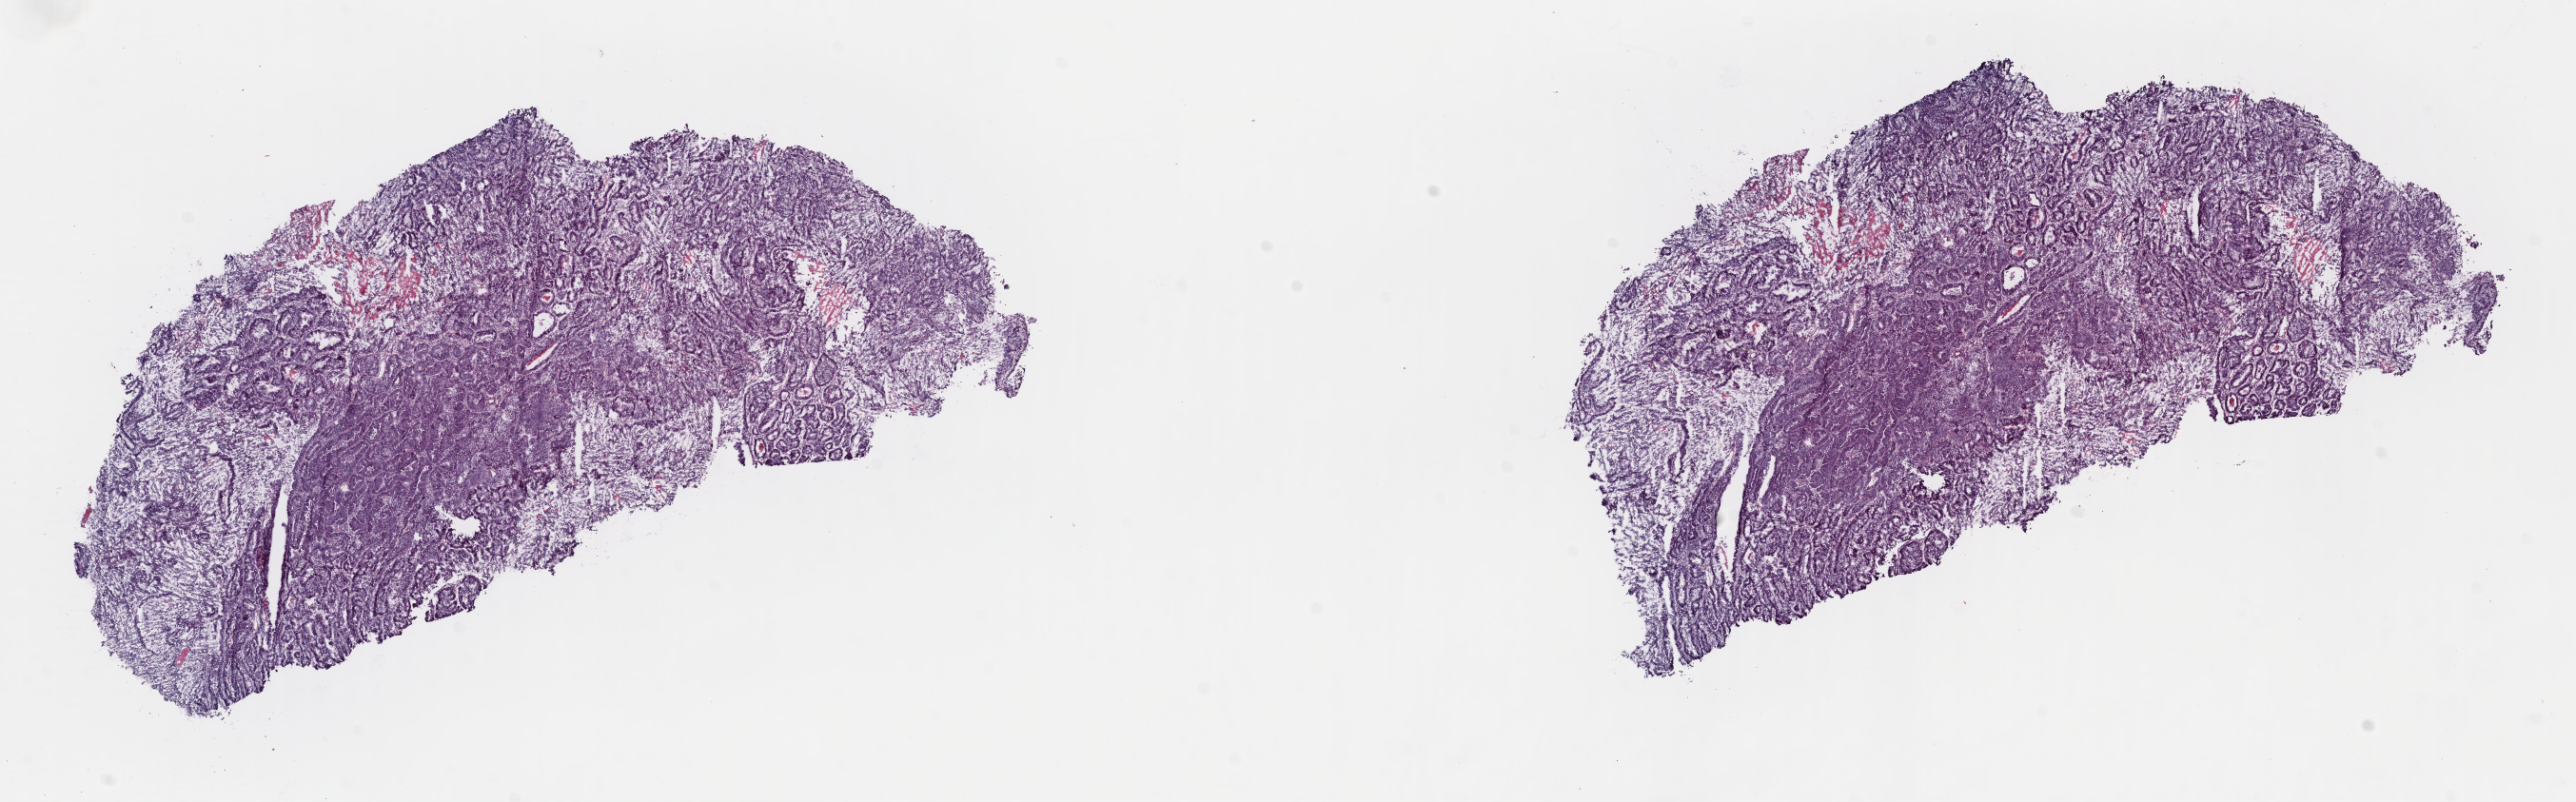
Whole-slide histology image, H&E-stained, a low-resolution overview of the entire scanned area, about 21.3 x 6.6 mm (from a 40x scan), frozen section from the top of the tissue portion, primary tumour sample from the uterus. Female patient; age at initial diagnosis 83 years. Pathologist review of this section (percent, as recorded): tumour cells 100%, tumour nuclei 80%.
Pathologic diagnosis: Endometrioid adenocarcinoma, NOS.